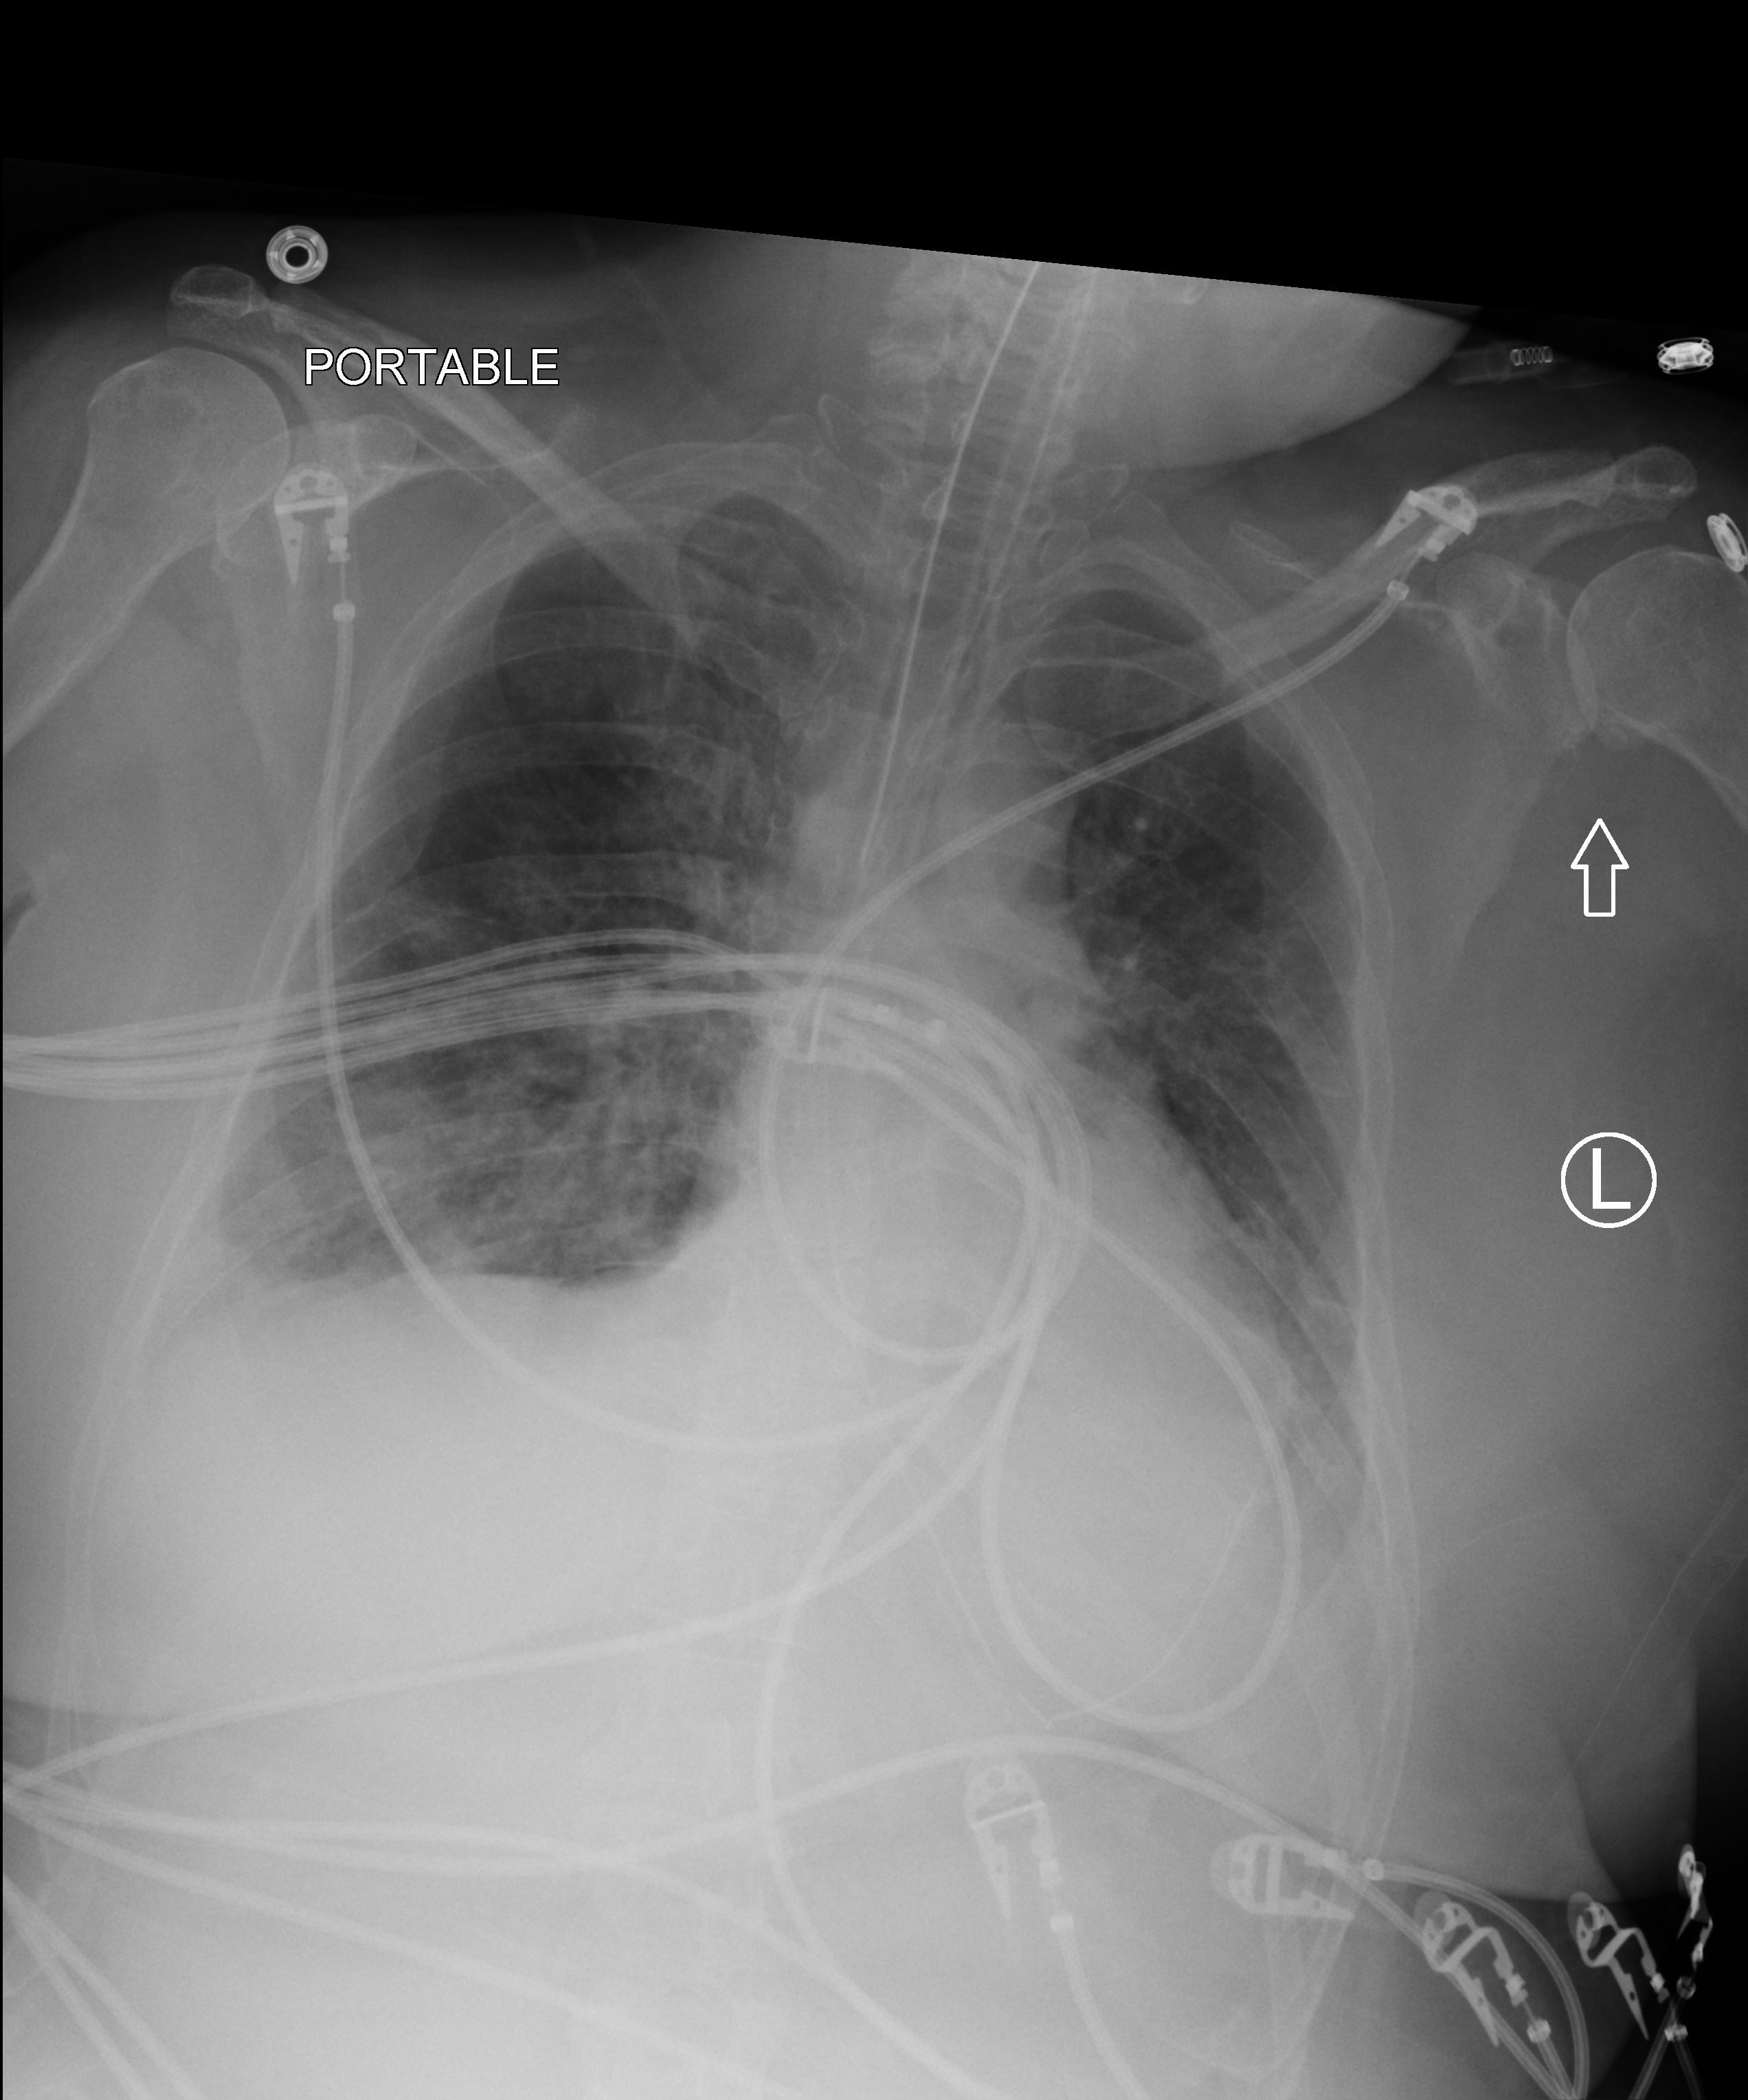
Portable chest radiograph; anteroposterior (AP) projection. Patient hospitalised with COVID-19, aged 18–59 years.
Hospital-stay facts (about this admission, not read from this image; timing relative to this image not recorded):
- admitted to intensive care during this hospital stay: yes